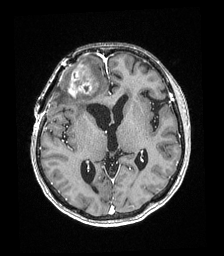
Brain MRI from a brain-tumour surgery series, one axial slice; position 100 of 192 along the scan axis; T1-weighted post-contrast; 1 mm slice thickness; 224 × 256 image matrix. From the clinical record (not read from this slice): histopathology: Astrocytoma; WHO grade: 4; IDH mutation: yes; tumour location: Right superficial frontal.
Outlined on this slice (manually delineated by an expert):
- tumour: box from (x=68, y=61) to (x=98, y=97) px